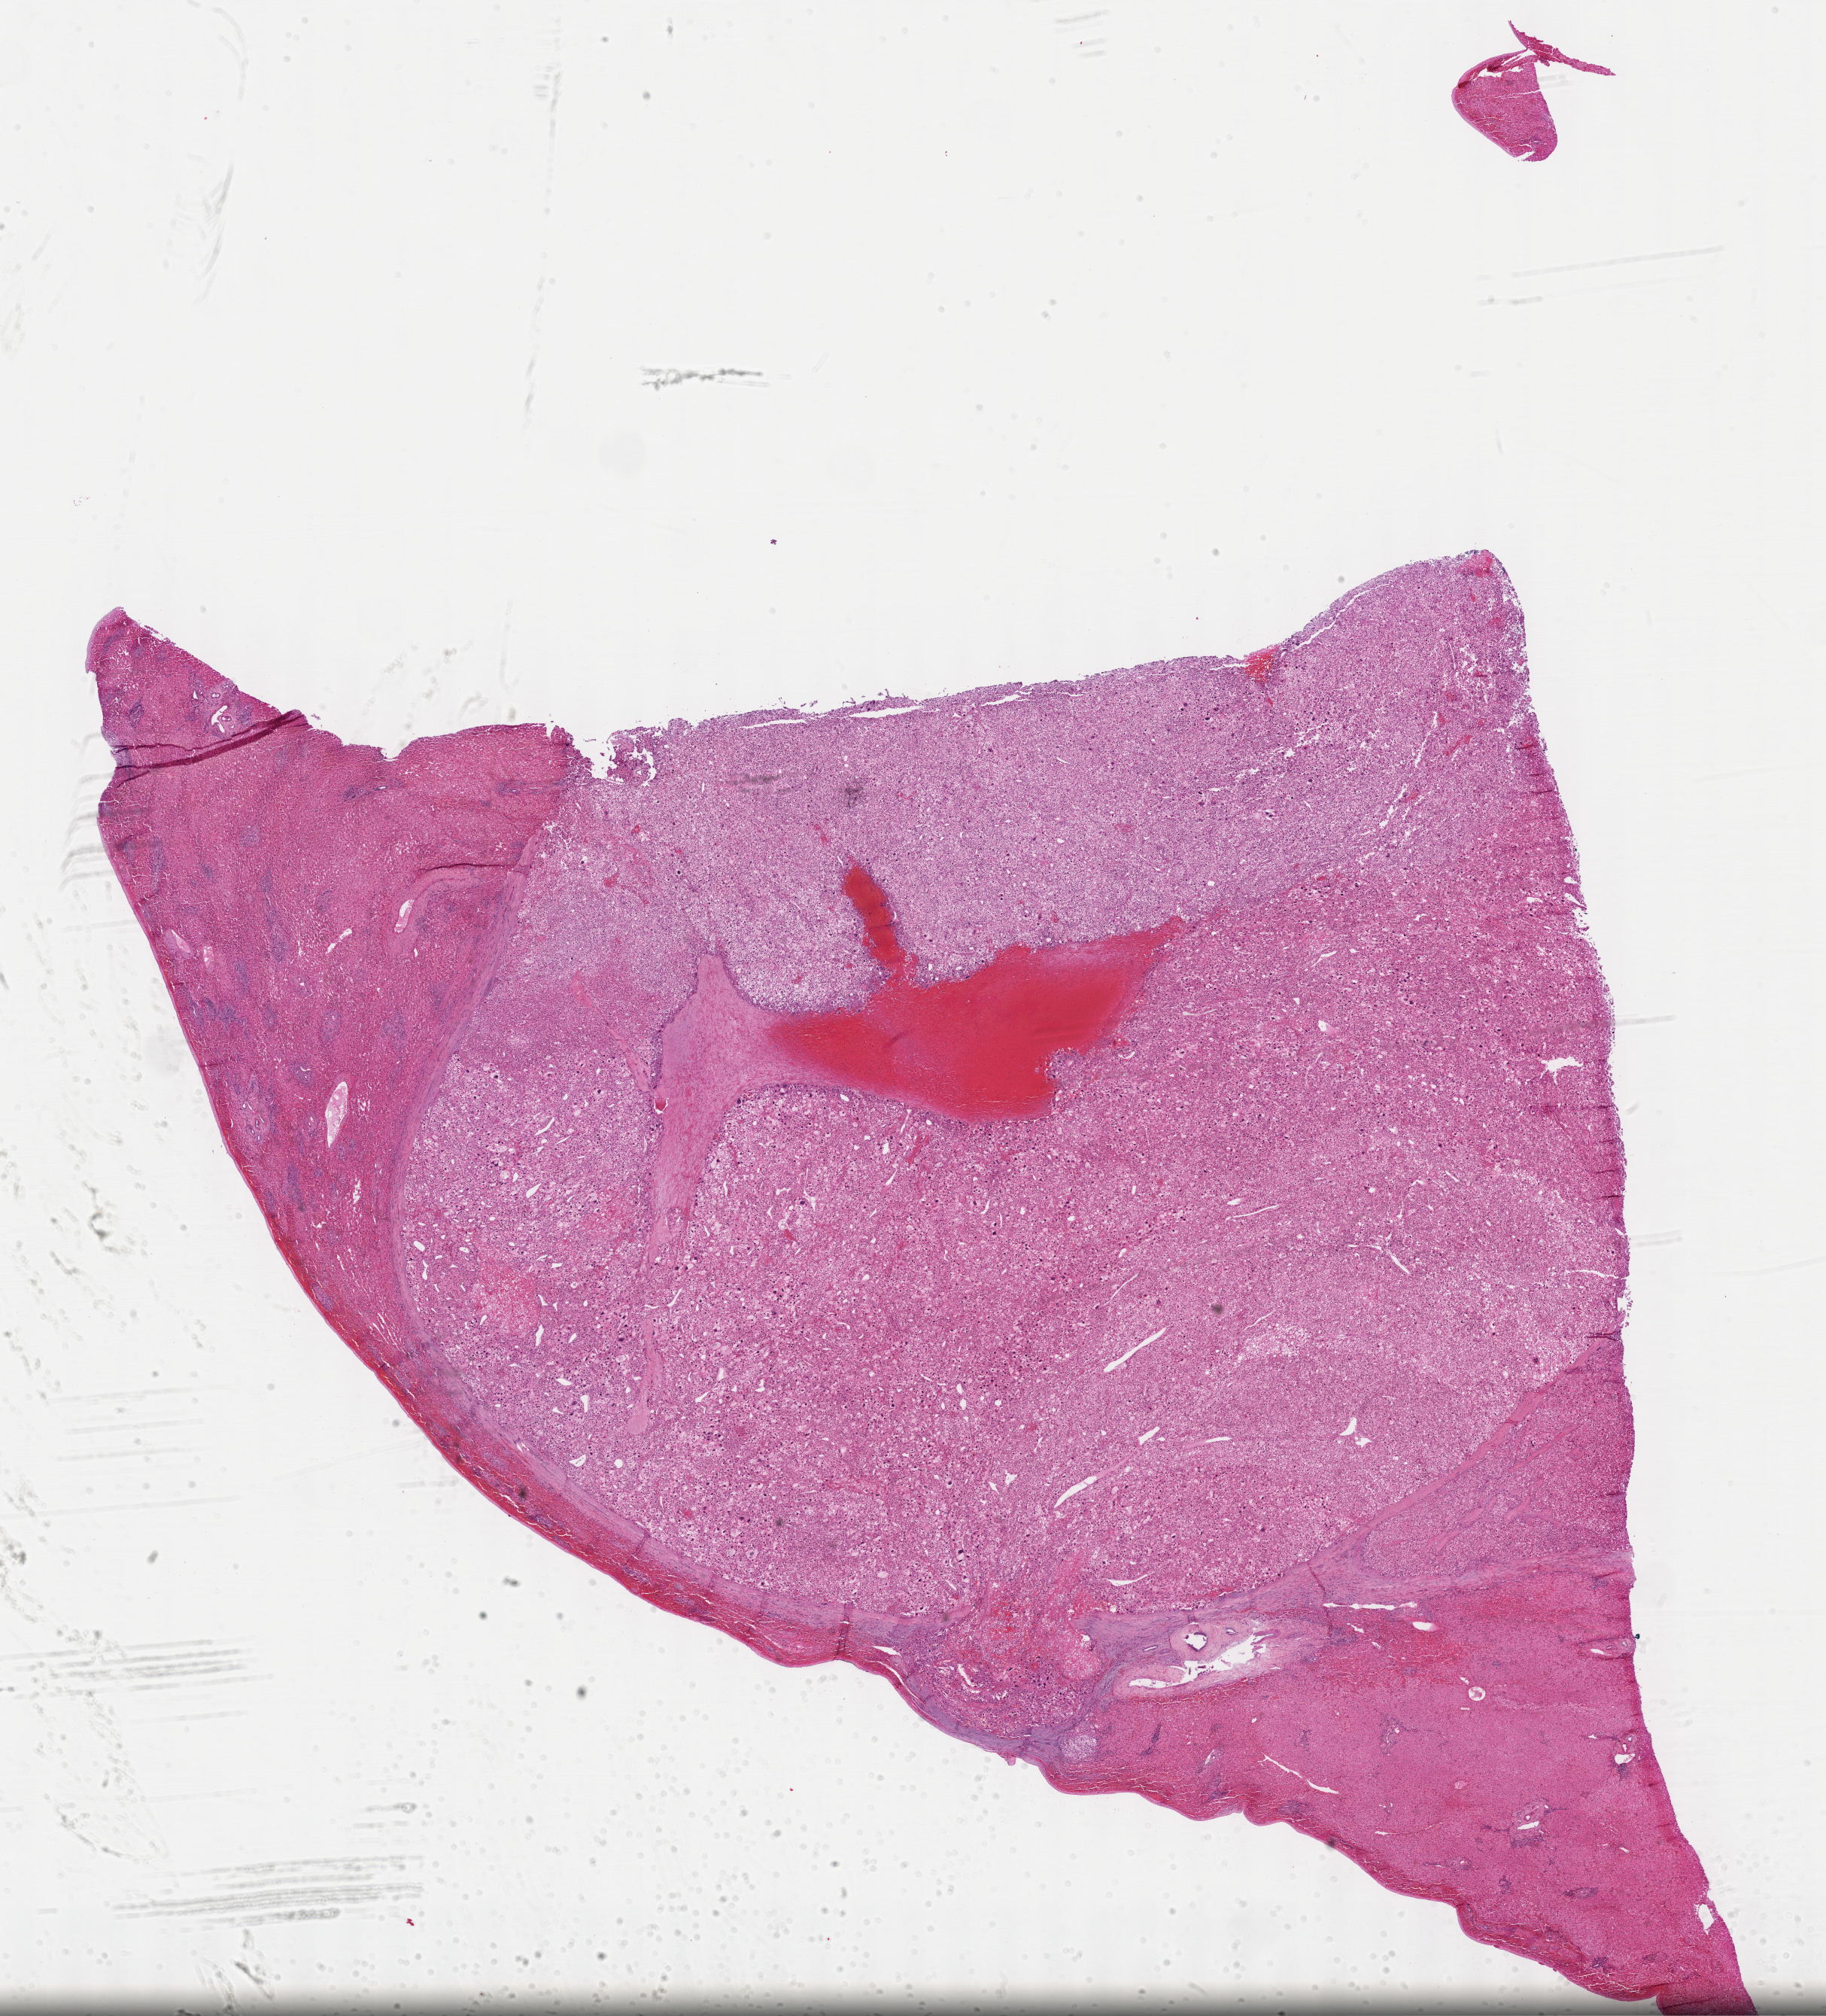
Digitized H&E-stained tissue section (whole slide), low-resolution overview of the scanned area, about 19.6 x 21.7 mm (acquisition: 40x scan). Formalin-fixed paraffin-embedded (FFPE) diagnostic section. Liver, primary tumour sample. Patient: female, age at initial diagnosis 68 years. Histologic grade: G2 (moderately differentiated).
• histologic diagnosis: Clear cell adenocarcinoma, NOS
• AJCC pathologic stage: I (7th edition)
• TNM: T1 NX MX